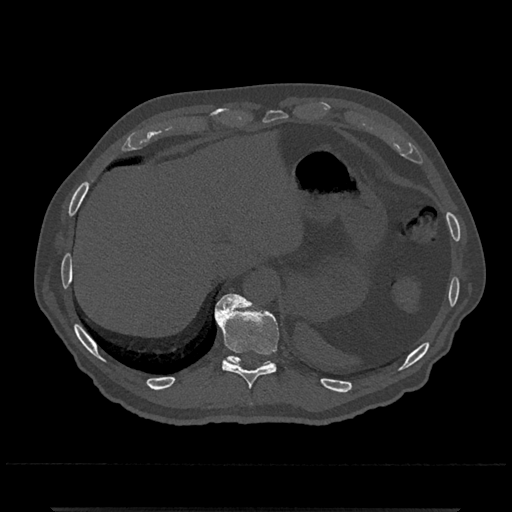
CT including the spine, one axial slice. Slice 541 of 797 in the series (ordered by position). Bone window (W 1800 / L 400 HU). 512 × 512 image matrix, field of view 393 × 393 mm. Male patient, age 67 years. From the clinical record (not read from this slice): primary cancer: prostate.
Structures marked on this image (semi-automatic segmentation, software-assisted and operator-edited):
- T10 vertebra: bounding box <214,293,279,389> (left, top, right, bottom; pixels)
- T11 vertebra: <224,356,272,367>